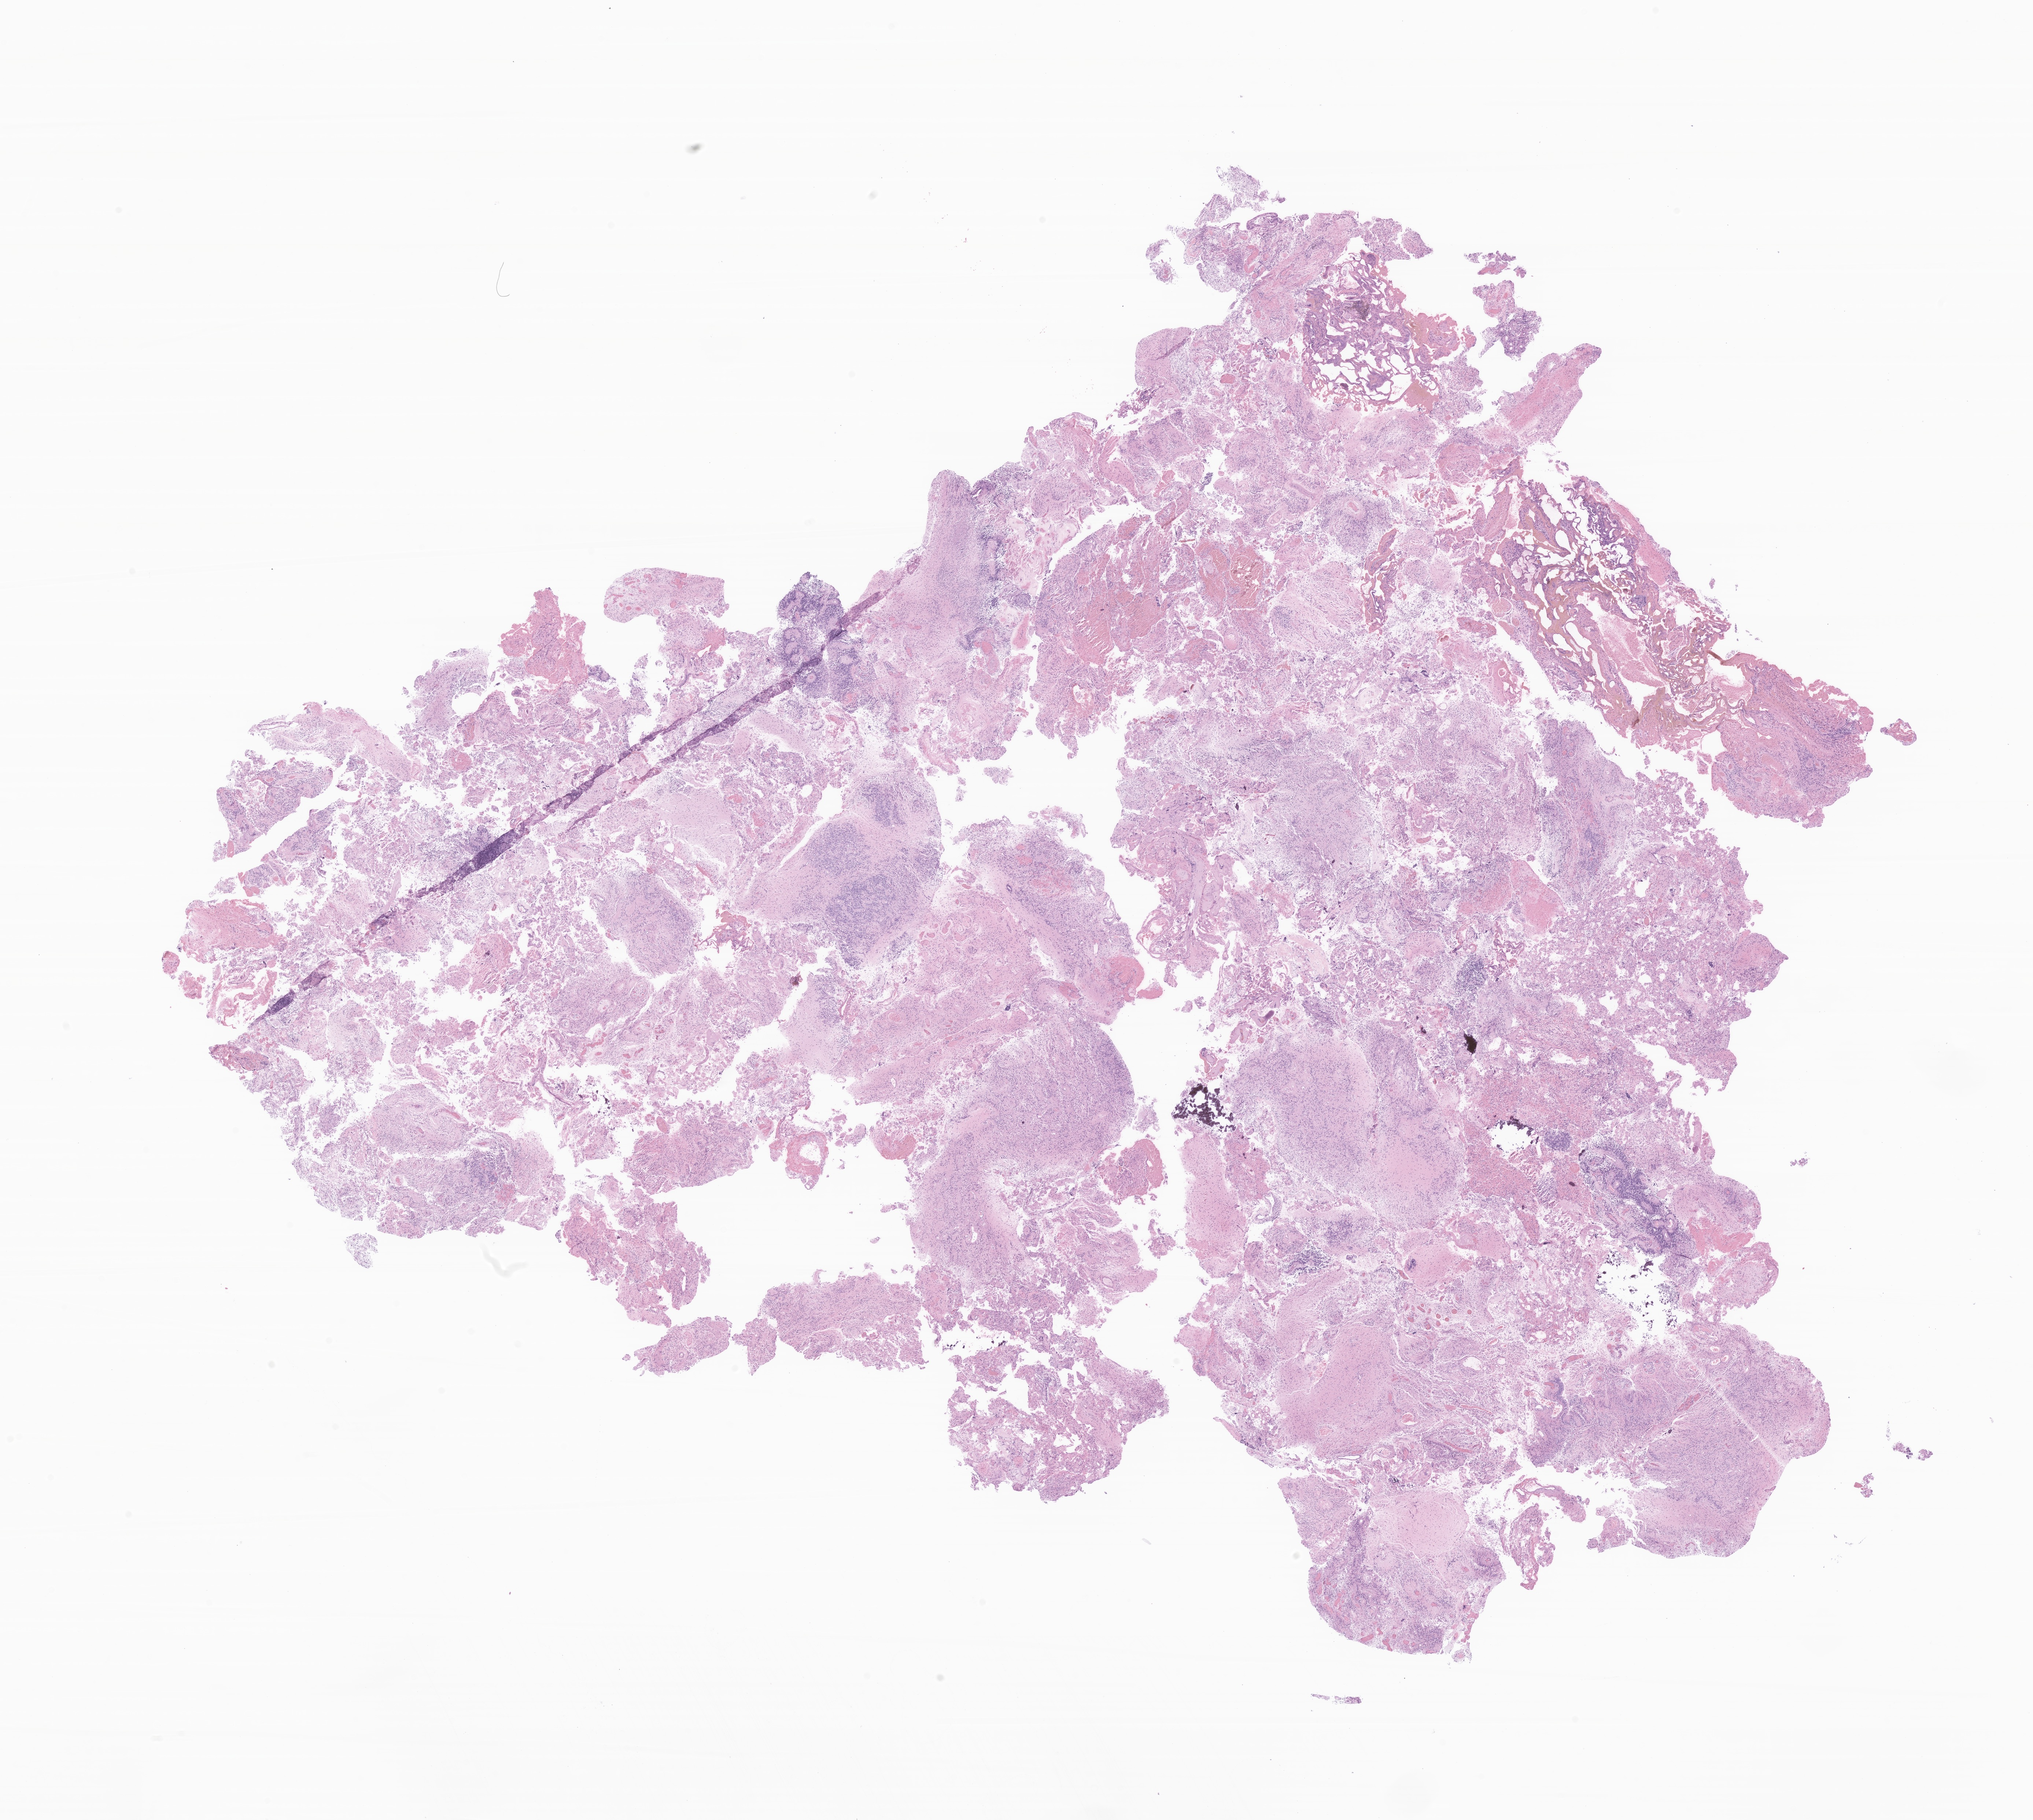
Digitized hematoxylin and eosin (H&E)-stained section of tumor tissue from the brain — shown as a low-resolution overview of the whole scanned area (about 23.4 x 20.9 mm). FFPE section. Female patient, age 70 months (5 years 10 months).
Diagnosis: Neoplasm, malignant.